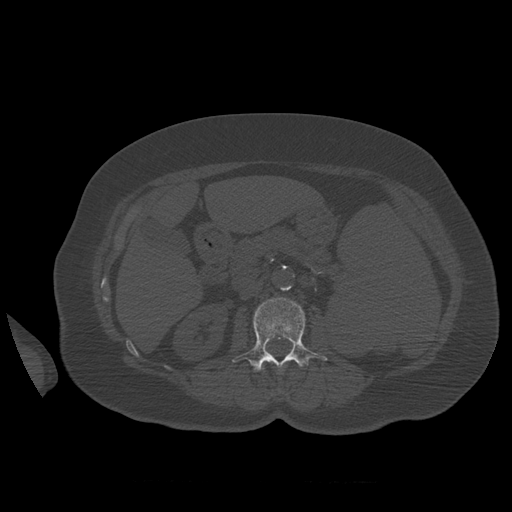
CT including the spine, one axial slice; position 256 of 399 along the scan axis; reconstruction kernel STANDARD; 120 kVp; bone window (W 1800 / L 400 HU); 1.25 mm slice thickness; 512 × 512 image matrix, field of view 404 × 404 mm. Patient age 81 years. Case-level facts recorded for this patient, not image findings: primary cancer: renal.
Structures marked on this image (semi-automatic segmentation, software-assisted and operator-edited):
- L1 vertebra: box from (x=260, y=366) to (x=265, y=371) px
- L2 vertebra: (x=232, y=298)–(x=328, y=372)